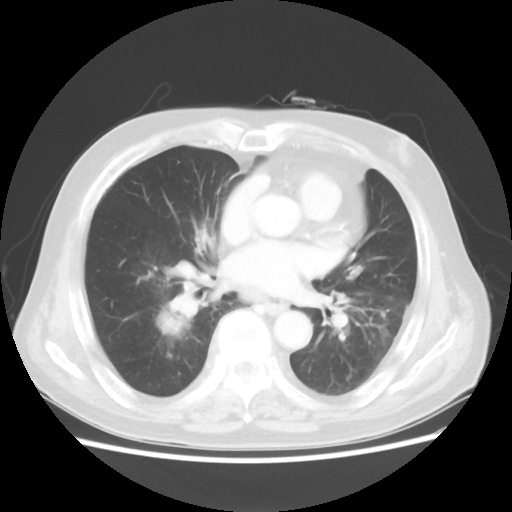
Chest CT, one axial slice; slice 17 of 44 in the series (ordered by position); 100 kVp; lung window (W 1500 / L -600 HU); 5 mm slice thickness; 512 × 512 image matrix, field of view 359 × 359 mm. Male patient, age 83 years. From the clinical record (not read from this slice): clinical TNM (as recorded): T2 N3 M0.
Annotated regions visible in this slice (bounding box drawn by a radiologist):
- lung tumour (recorded histology: adenocarcinoma): box from (x=144, y=294) to (x=192, y=353) px